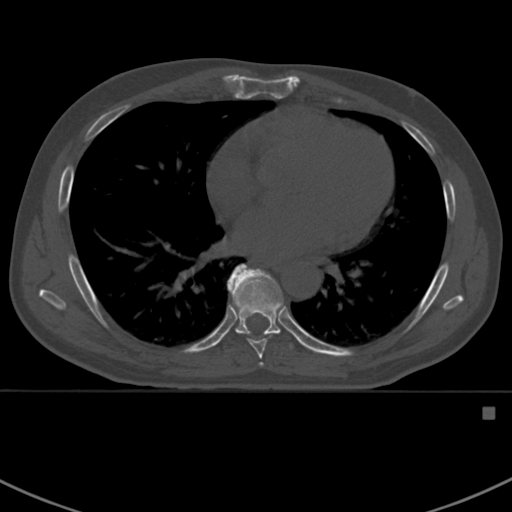
CT including the spine, one axial slice; slice 408 of 412 in the series (ordered by position); 120 kVp; bone window (W 1800 / L 400 HU); 1.5 mm slice thickness; 512 × 512 image matrix, field of view 358 × 358 mm. Male patient, age 59 years. Case-level facts recorded for this patient, not image findings: primary cancer: prostate.
Outlined on this slice (semi-automatically segmented with operator editing):
- T7 vertebra: bounding box <228,281,272,367> (left, top, right, bottom; pixels)
- T8 vertebra: <229,264,294,350>